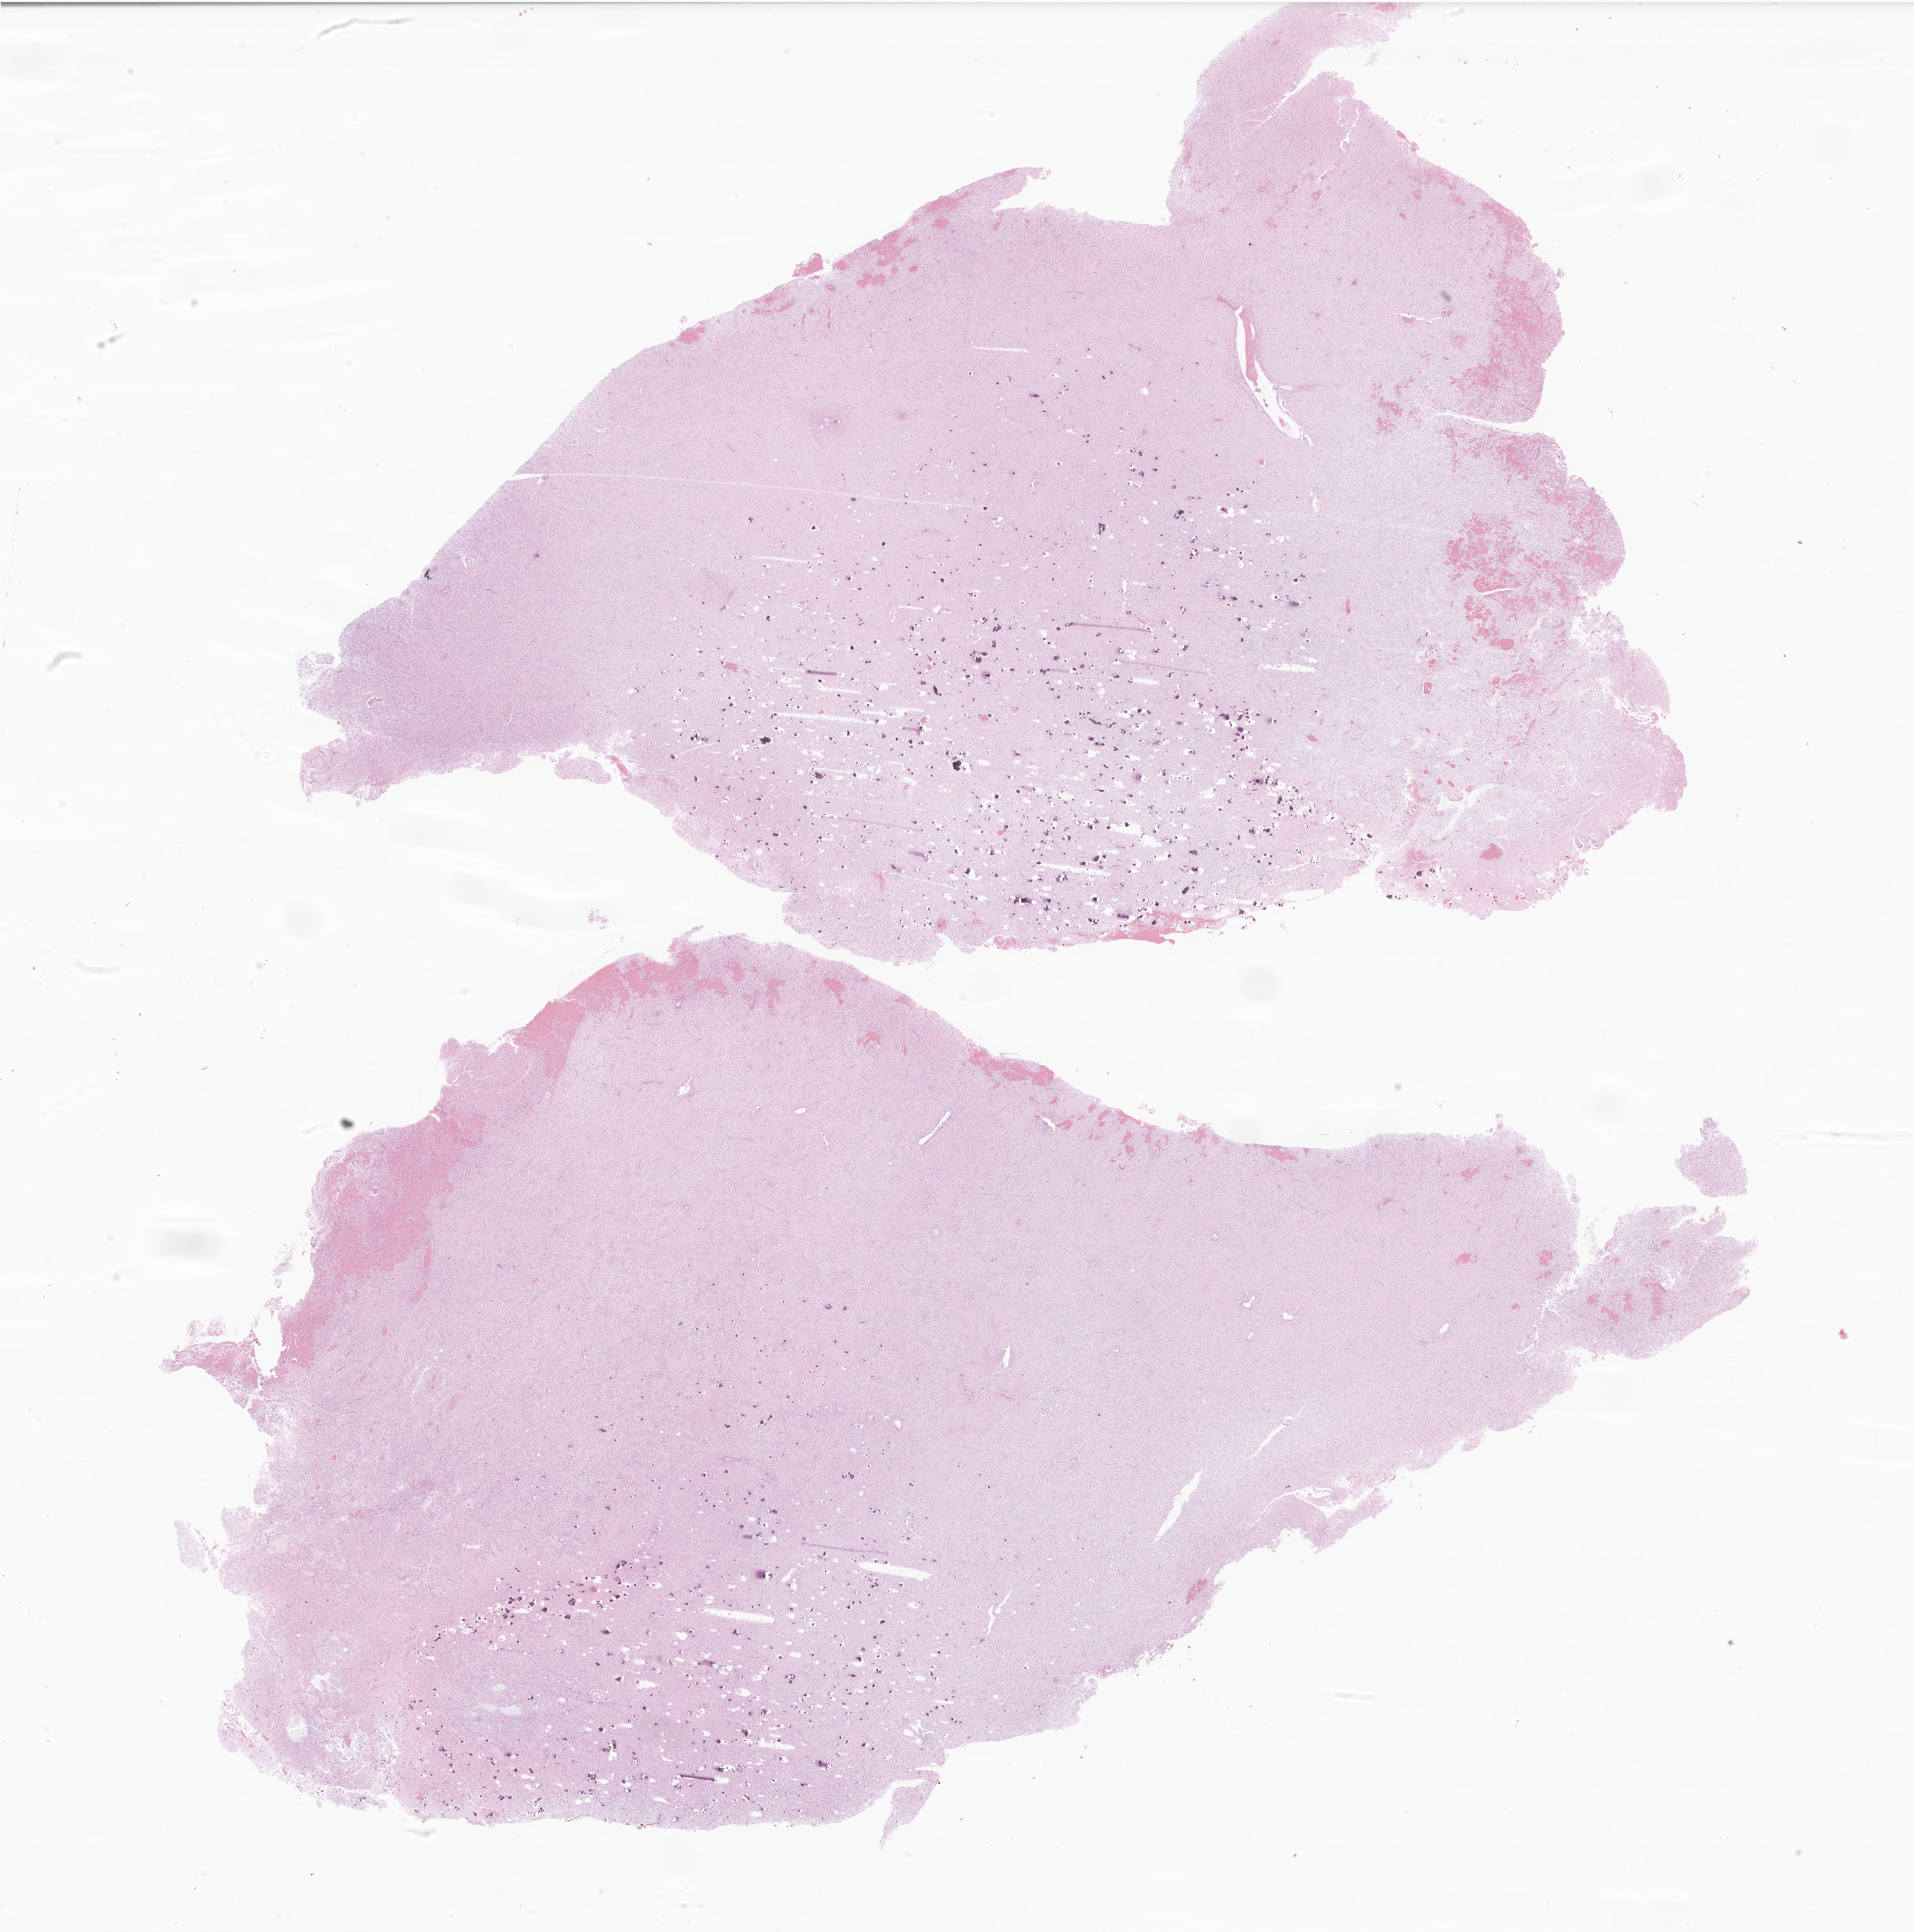
Digitized haematoxylin and eosin-stained section of tumor tissue from the cerebellum — low-resolution overview of the scanned area, about 23.0 x 23.2 mm, formalin-fixed paraffin-embedded section. Patient: male, age 179 months (14 years 11 months).
Diagnosis: Pilocytic astrocytoma.